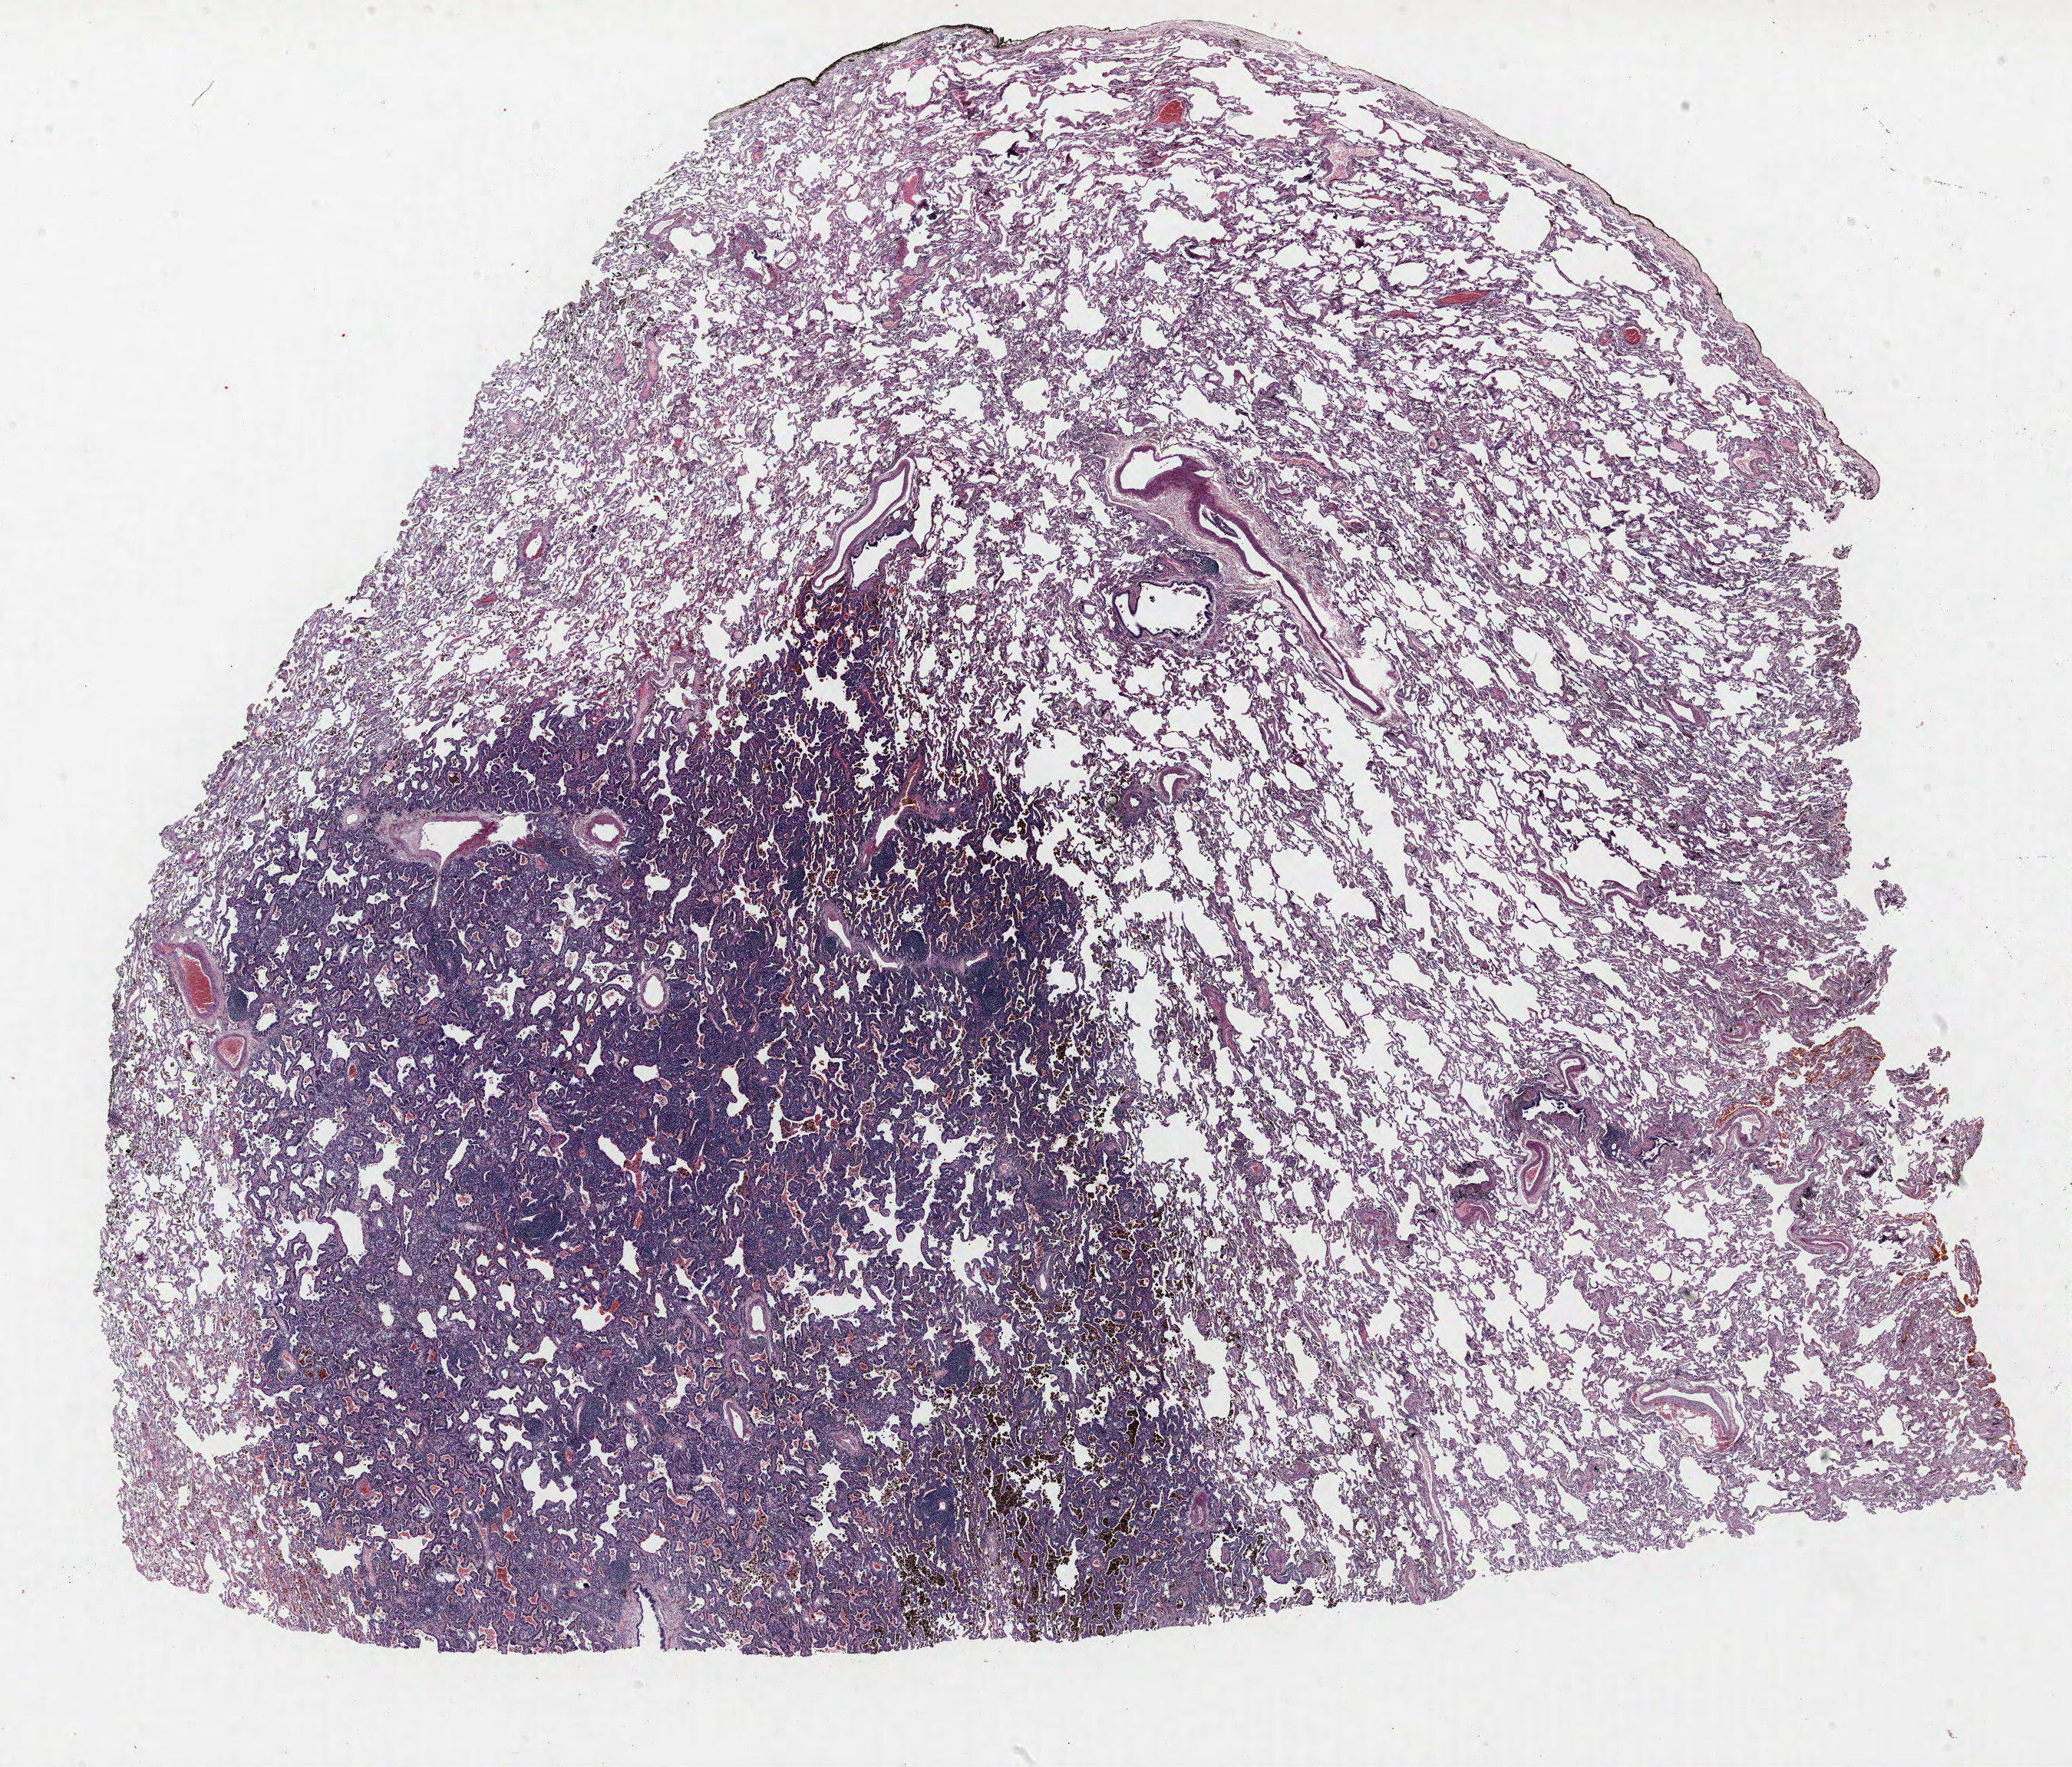
H&E whole-slide image — whole scanned area (about 21.6 x 18.4 mm, slide scanned at 40x) shown as a low-resolution overview. Formalin-fixed paraffin-embedded (FFPE) section. Lung tissue. Male, age 60 at enrolment. Former smoker at enrolment. Grade: well differentiated (G1).
* tumour size (pathology): 16 mm
* stage (AJCC 6th edition): IA
* participant's lung-cancer diagnosis: Bronchiolo-alveolar carcinoma, non-mucinous (ICD-O-3 8252/3)
* primary tumour location (clinical record): left upper lobe